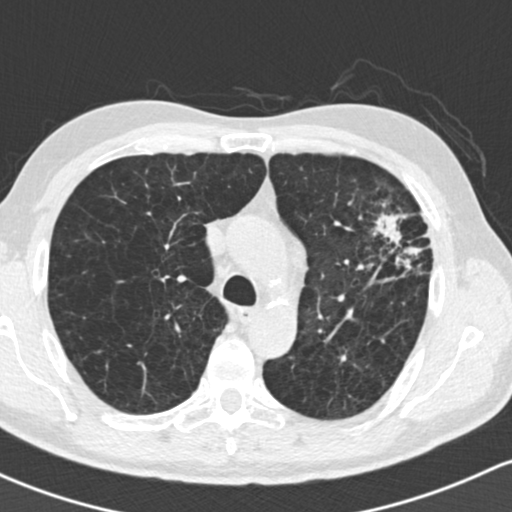
Low-dose screening chest CT, one axial slice. Position 110 of 162 along the scan axis. Reconstruction kernel B30f. Lung window (W 1500 / L -600 HU). 2 mm slice thickness. 512 × 512 image matrix, field of view 318 × 318 mm.
Annotated regions visible in this slice (outlined manually by an expert reader):
- lesion 1 (tumor, upper lobe of left lung): bounding box (x1, y1, x2, y2) in pixels: (373, 213, 421, 270)